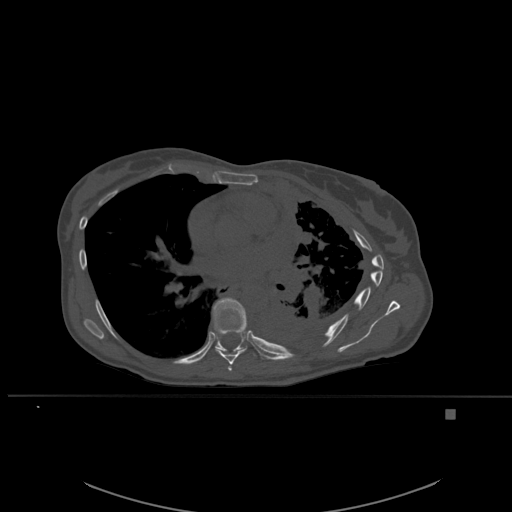
CT including the spine, one axial slice; slice 360 of 537 in the series (ordered by position); bone window (W 1800 / L 400 HU); 1.5 mm slice thickness; 512 × 512 image matrix. Patient: female, 45 years. From the clinical record (not read from this slice): primary cancer: lung.
Outlined on this slice (semi-automatic segmentation, software-assisted and operator-edited):
- T6 vertebra: bounding box [x1, y1, x2, y2] px = [228, 364, 232, 371]
- T7 vertebra: [215, 313, 248, 365]
- T8 vertebra: [212, 297, 247, 354]